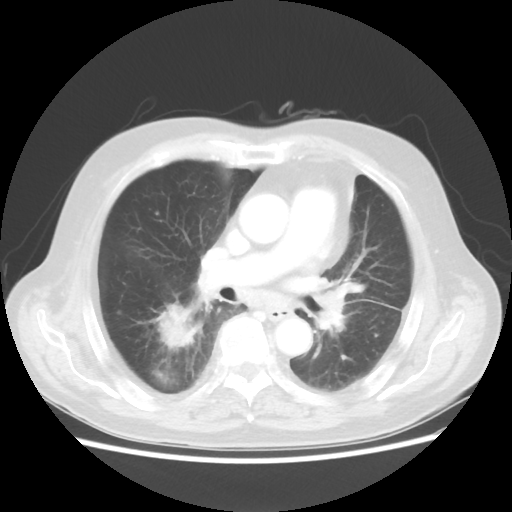
Chest CT, one axial slice; position 22 of 44 along the scan axis; 100 kVp; lung window (W 1500 / L -600 HU); 512 × 512 image matrix, field of view 359 × 359 mm. Male patient, age 83 years. From the clinical record (not read from this slice): clinical TNM (as recorded): T2 N3 M0.
Annotated regions visible in this slice (rectangle marked by the reading radiologist):
- lung tumour (recorded histology: adenocarcinoma): bounding box (x1, y1, x2, y2) in pixels: (142, 297, 200, 362)